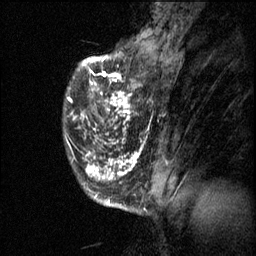
Breast MRI (dynamic contrast-enhanced), one sagittal slice. Position 13 of 60 along the scan axis. 3 images stored at this slice position (order not interpretable as contrast timing). 1.5 T. TE 4.2 ms, TR 11.1 ms. 2 mm slice thickness. 256 × 256 image matrix, field of view 180 × 180 mm. Patient: female, 50 years.
Structures marked on this image (semi-automatically segmented with operator editing):
- analysis volume of interest (the breast-tissue region the enhancement analysis was run in; not a lesion): bounding box [x1, y1, x2, y2] px = [68, 68, 153, 141]
- tumour enhancement mask (voxels above the 70 % enhancement threshold inside the analysis volume of interest): [68, 68, 148, 141]